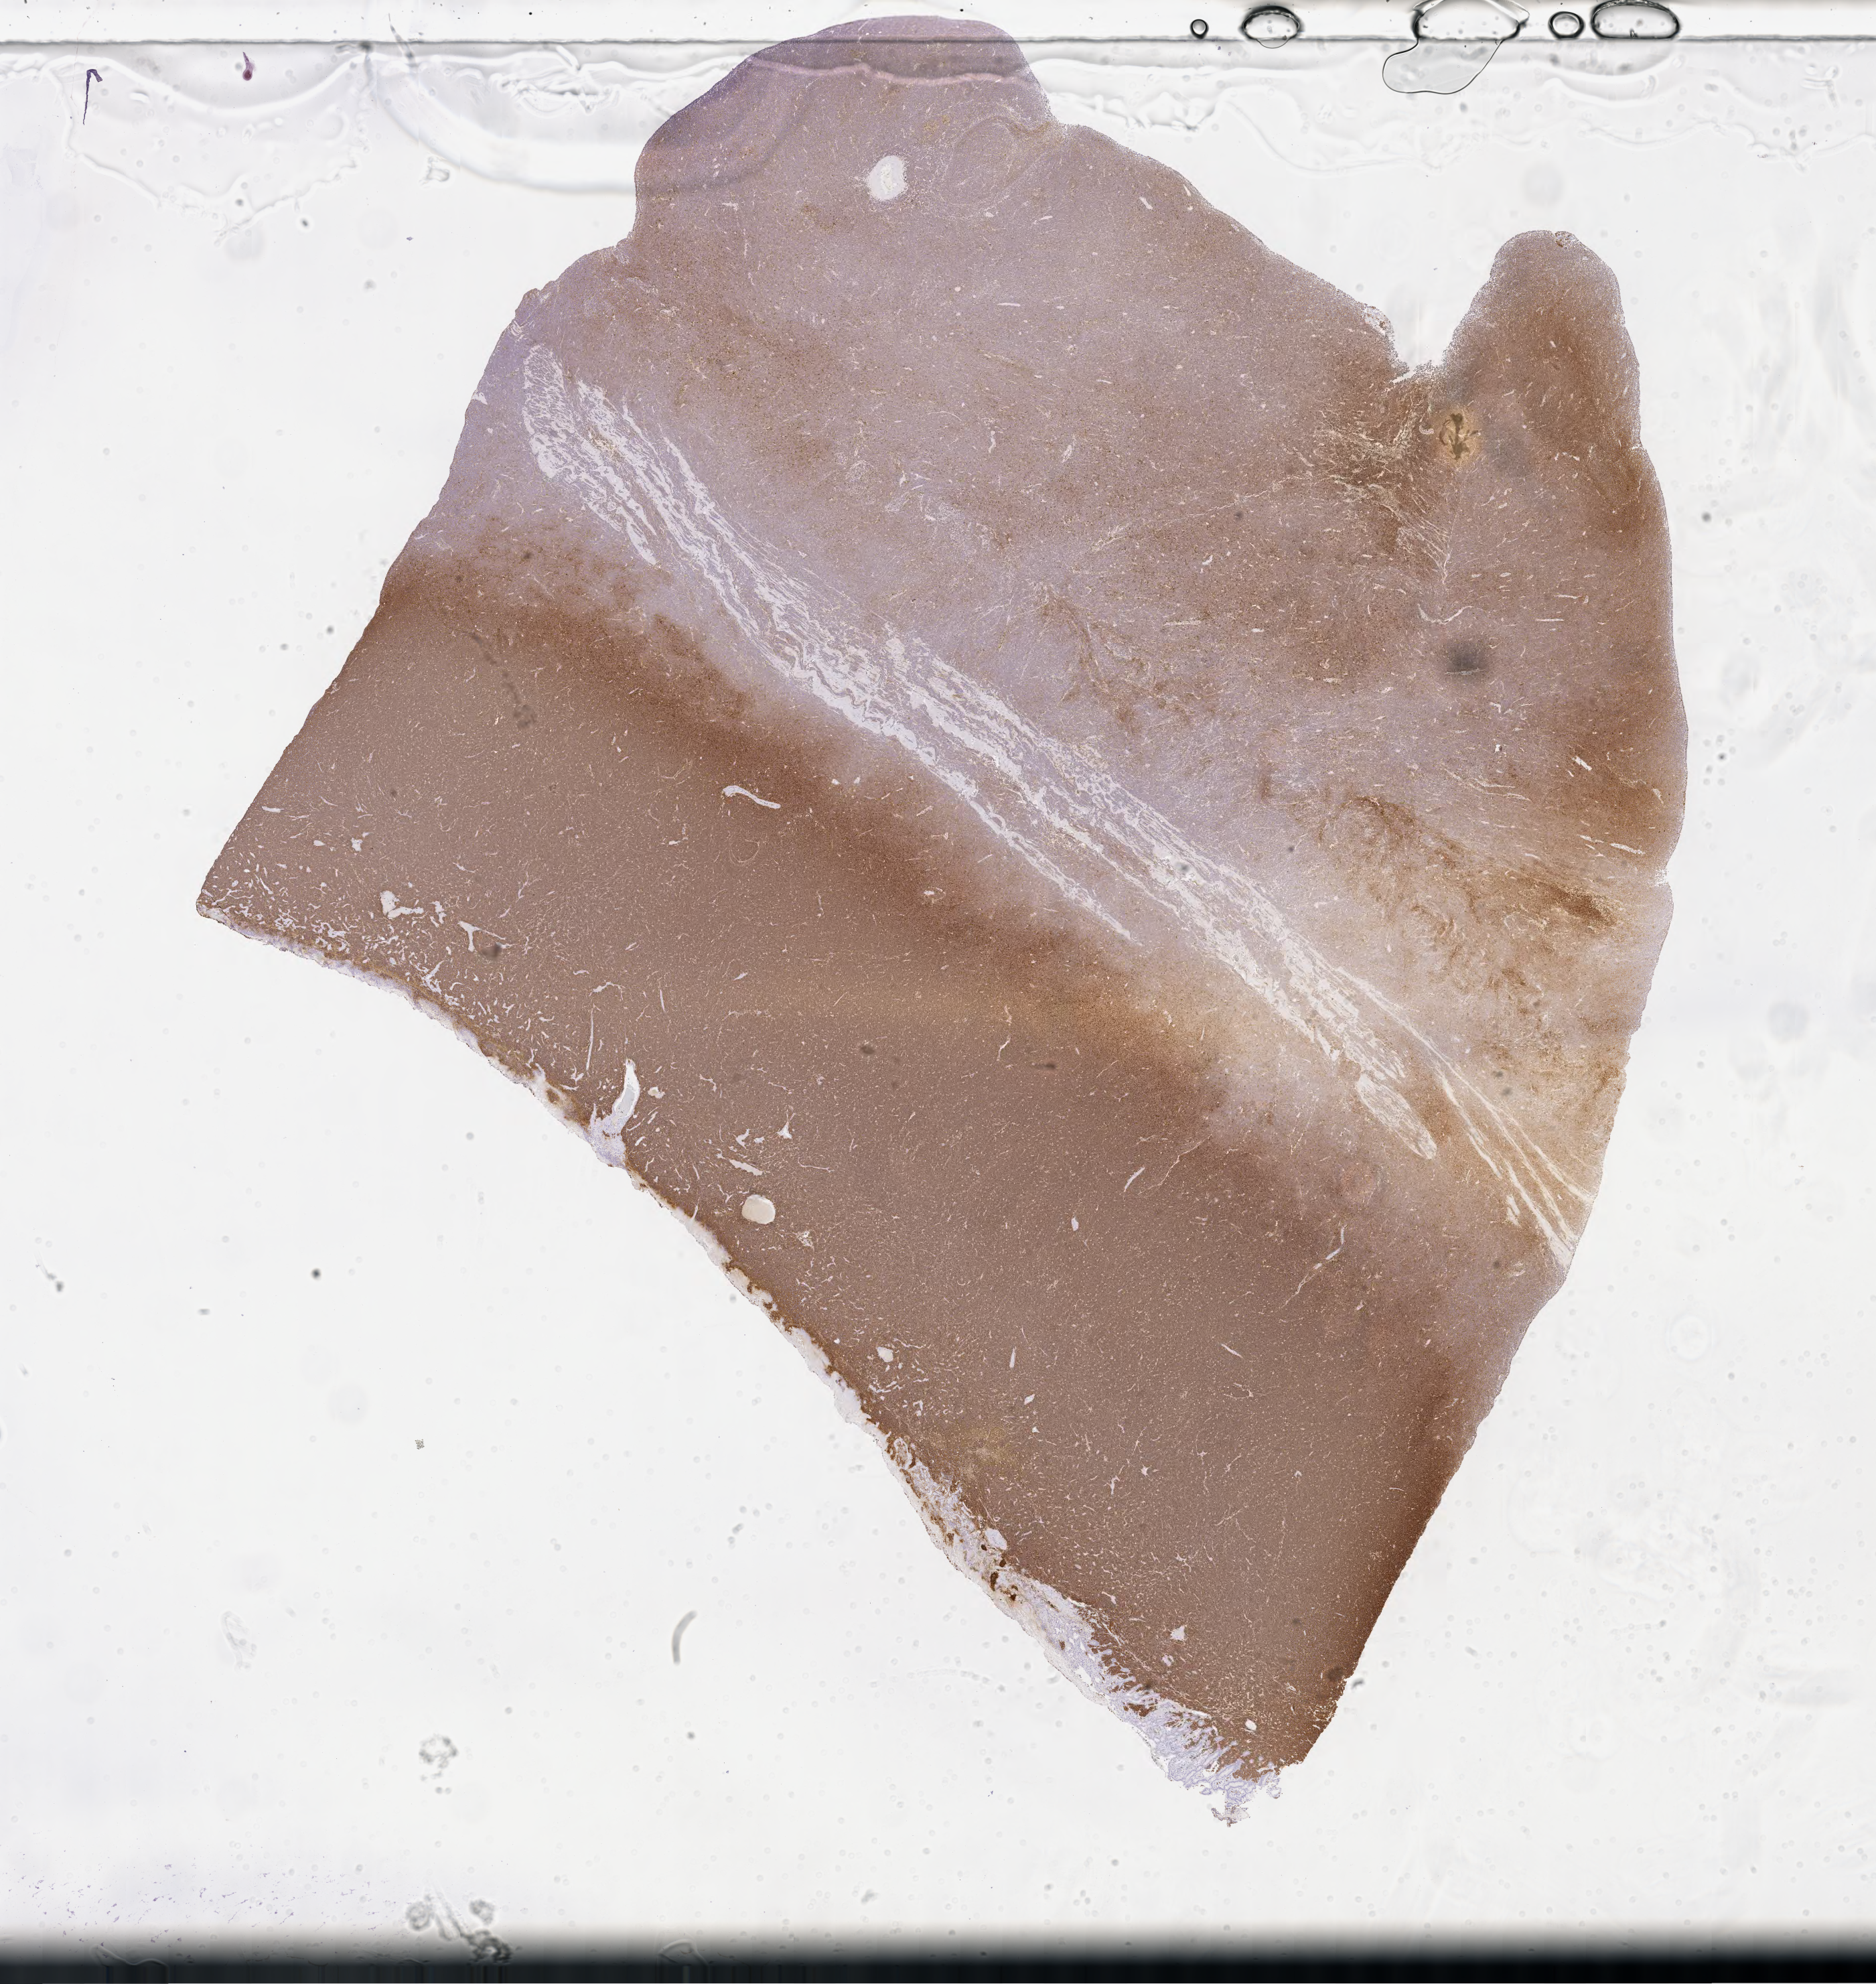
Whole-slide image, immunohistochemical stain for CD20, a low-resolution overview of the entire scanned area, about 22.6 x 23.9 mm. Specimen: tumor tissue. Male patient, aged 36.
Diagnosis: Burkitt lymphoma, NOS.